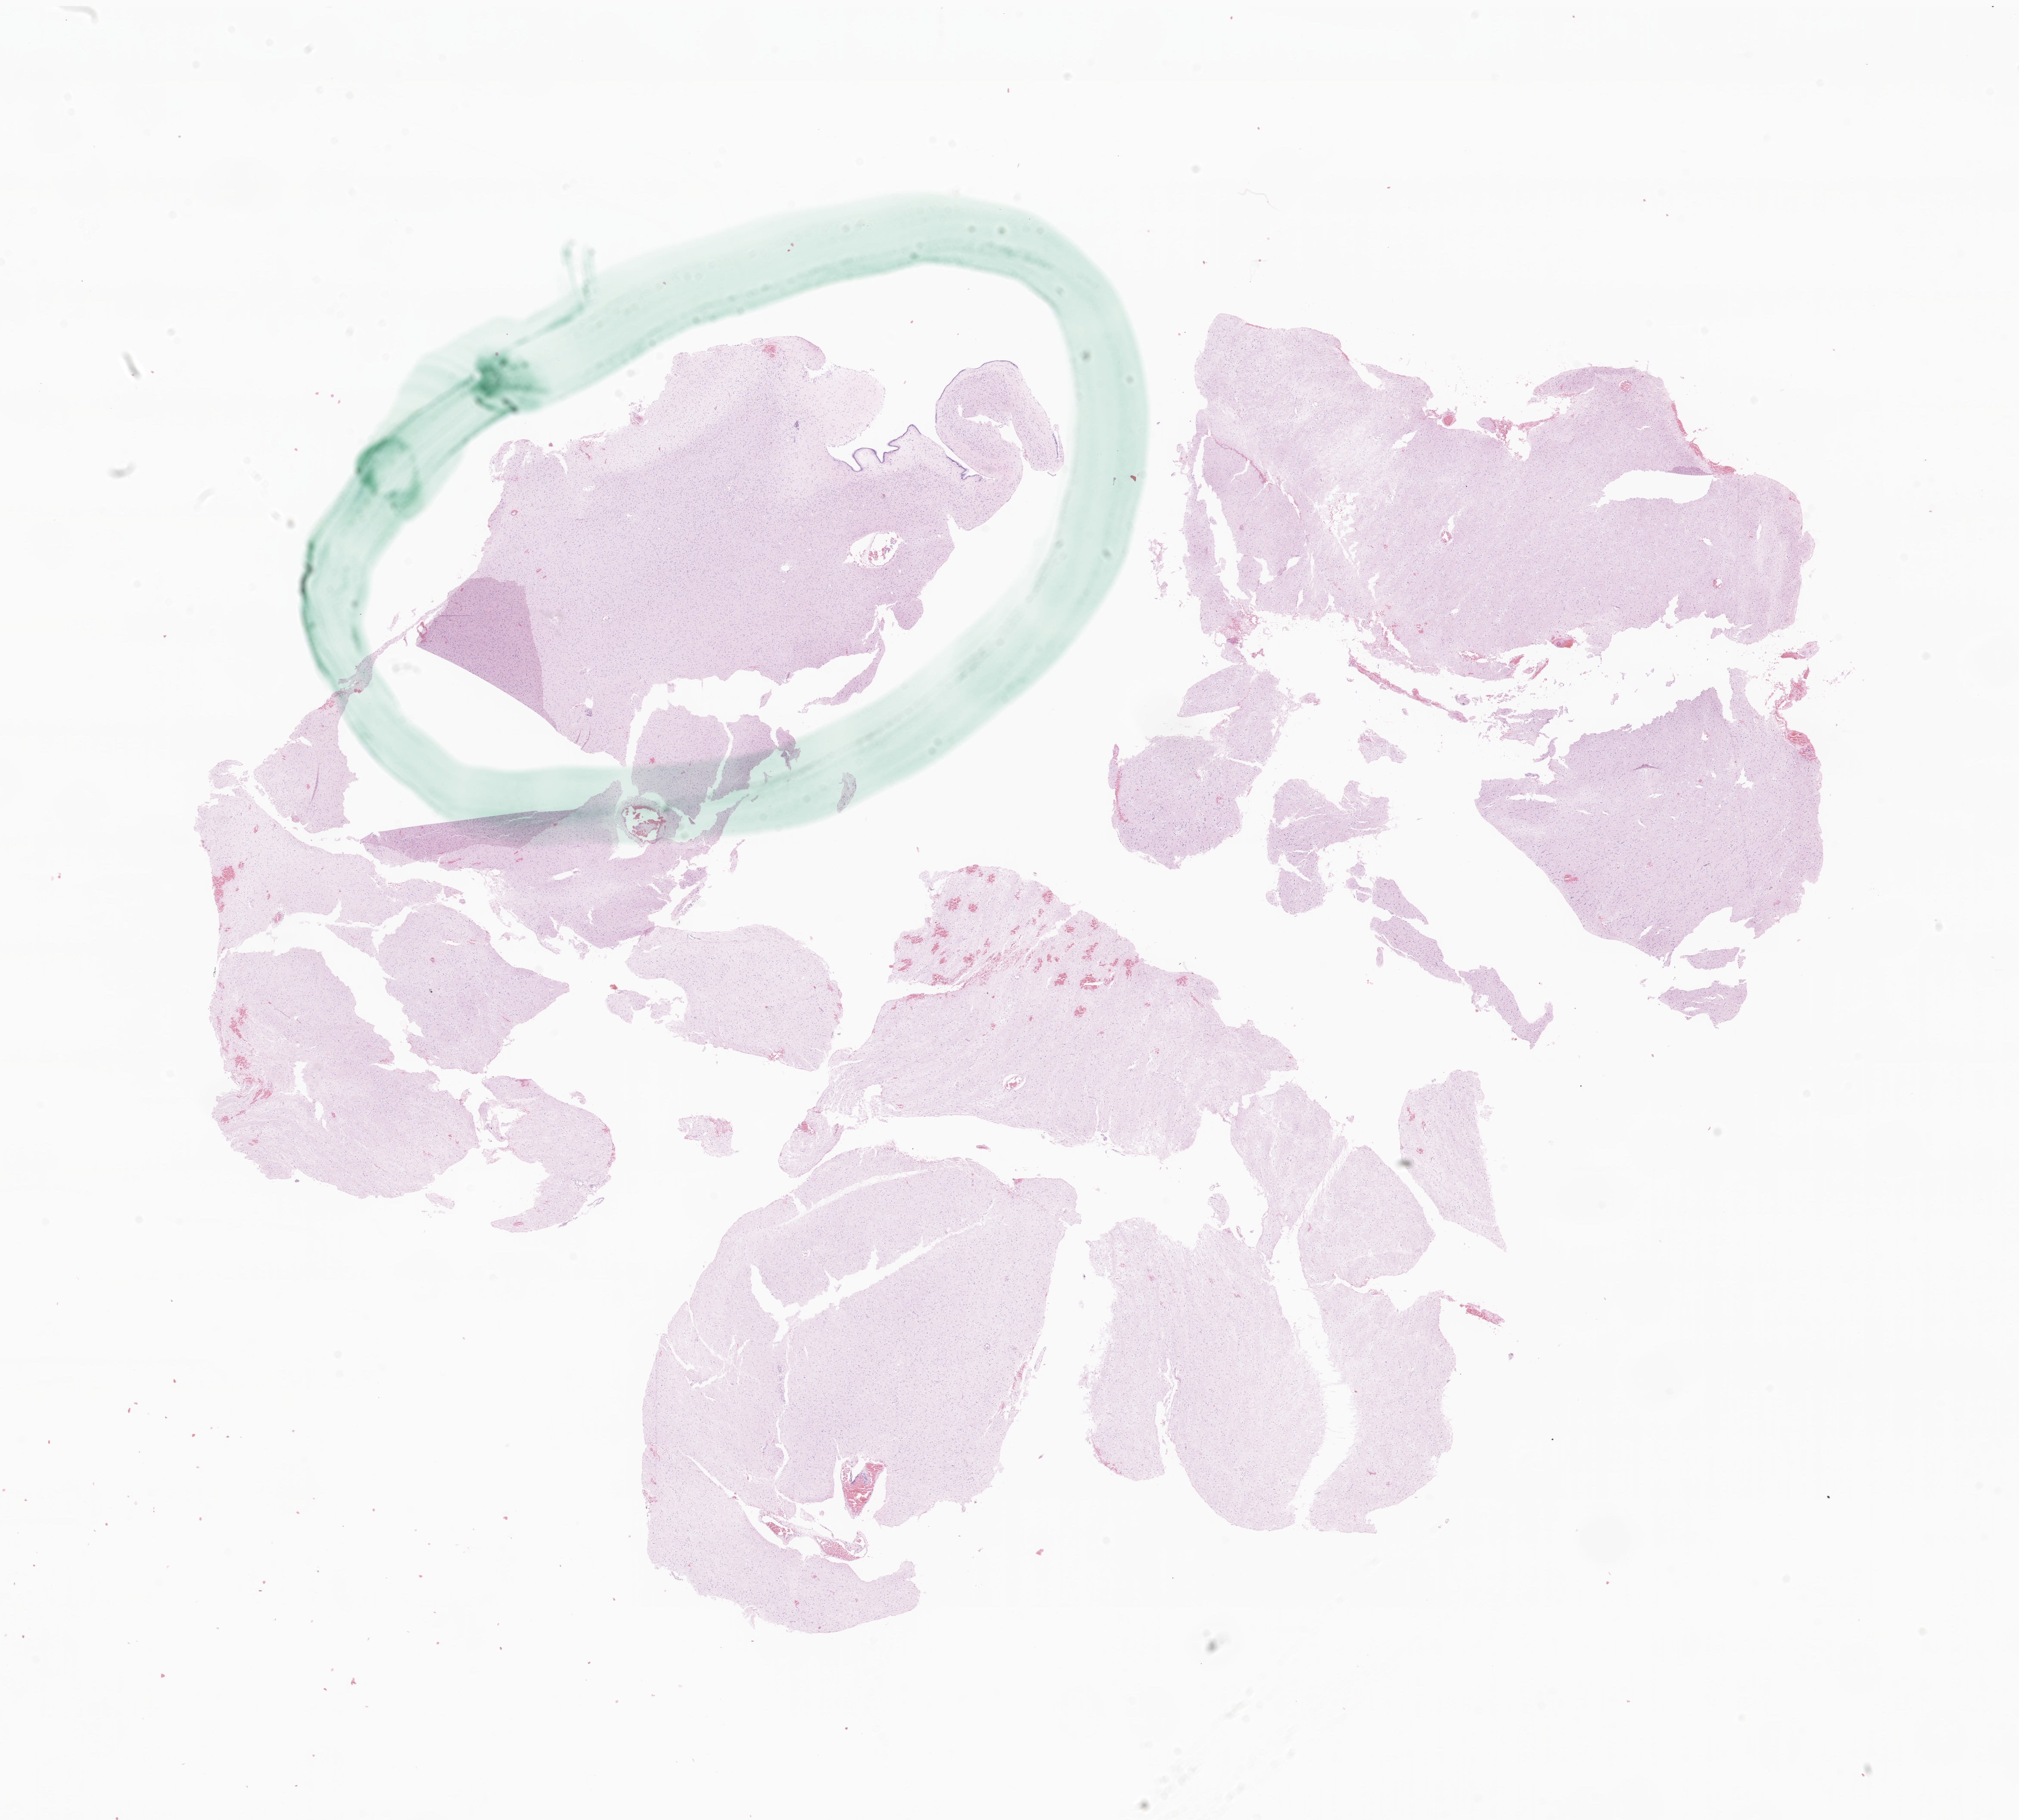
H&E whole-slide image of tumor tissue from the brain — whole scanned area (about 19.8 x 17.8 mm) shown as a low-resolution overview, FFPE section. Patient male; age 913 days (about 2.5 years).
Recorded diagnosis: Neoplasm, uncertain whether benign or malignant.